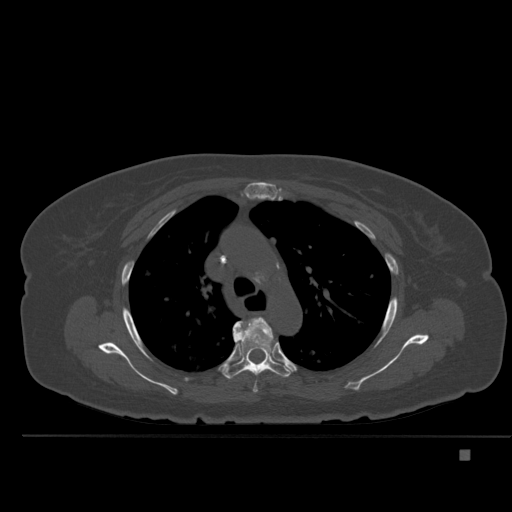
CT including the spine, one axial slice. Slice 358 of 477 in the series (ordered by position). Bone window (W 1800 / L 400 HU). 512 × 512 image matrix, field of view 422 × 422 mm. Female patient, age 74 years. From the clinical record (not read from this slice): primary cancer: colon.
Outlined on this slice (semi-automatic segmentation, software-assisted and operator-edited):
- T4 vertebra: bounding box (x1, y1, x2, y2) in pixels: (244, 317, 272, 393)
- T5 vertebra: (222, 317, 292, 379)